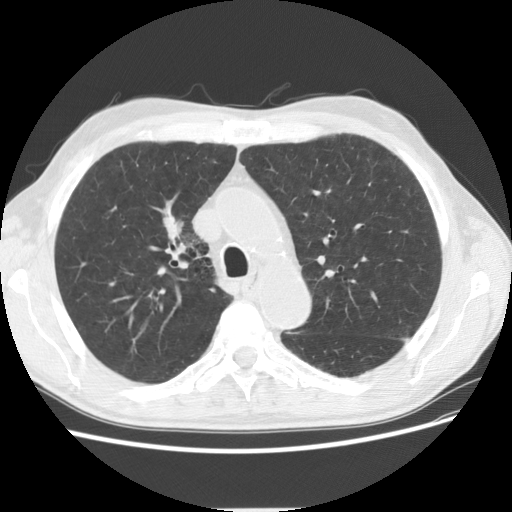
Chest CT (low-dose screening protocol), one axial image; first (baseline) screen; lung window (W 1500 / L -600 HU); standard (soft-tissue) reconstruction kernel (STANDARD); 120 kVp; slice 43 of 135 in the series; 512 × 512 image matrix. Male participant, aged 73 years at enrolment. Current smoker at enrolment.
- Expert reader's lesion annotation, box from (x=141, y=199) to (x=205, y=261) px.
- Screening reader's record for this exam (one nodule recorded; not confirmed to be the boxed lesion): non-calcified nodule or mass ≥4 mm, right upper lobe, 16 × 9 mm, spiculated (stellate) margins, soft tissue attenuation.
- Later outcome: lung cancer diagnosed 734 days after this screen (after the third annual screen) — squamous cell carcinoma, NOS, right upper lobe, poorly differentiated (G3), stage IIIB (AJCC 6th edition), 56 mm at pathology.